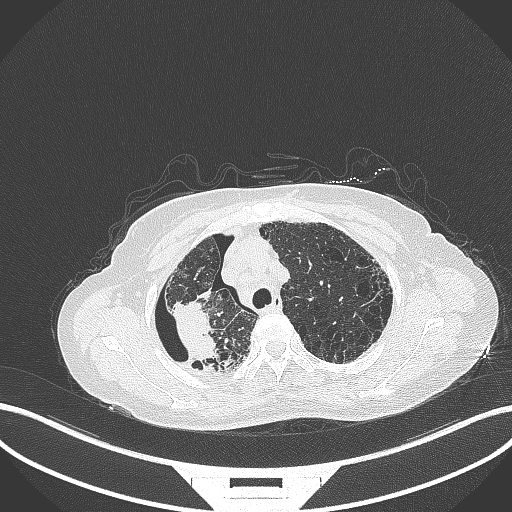
Chest CT, one axial slice; position 283 of 408 along the scan axis; reconstruction kernel B70f; 120 kVp; lung window (W 1500 / L -600 HU); 512 × 512 image matrix. Patient: female, 64 years. From the clinical record (not read from this slice): clinical TNM (as recorded): T3 N3 M0.
Outlined on this slice (rectangle marked by the reading radiologist):
- lung tumour (recorded histology: squamous cell carcinoma): bounding box (x1, y1, x2, y2) in pixels: (167, 288, 225, 368)